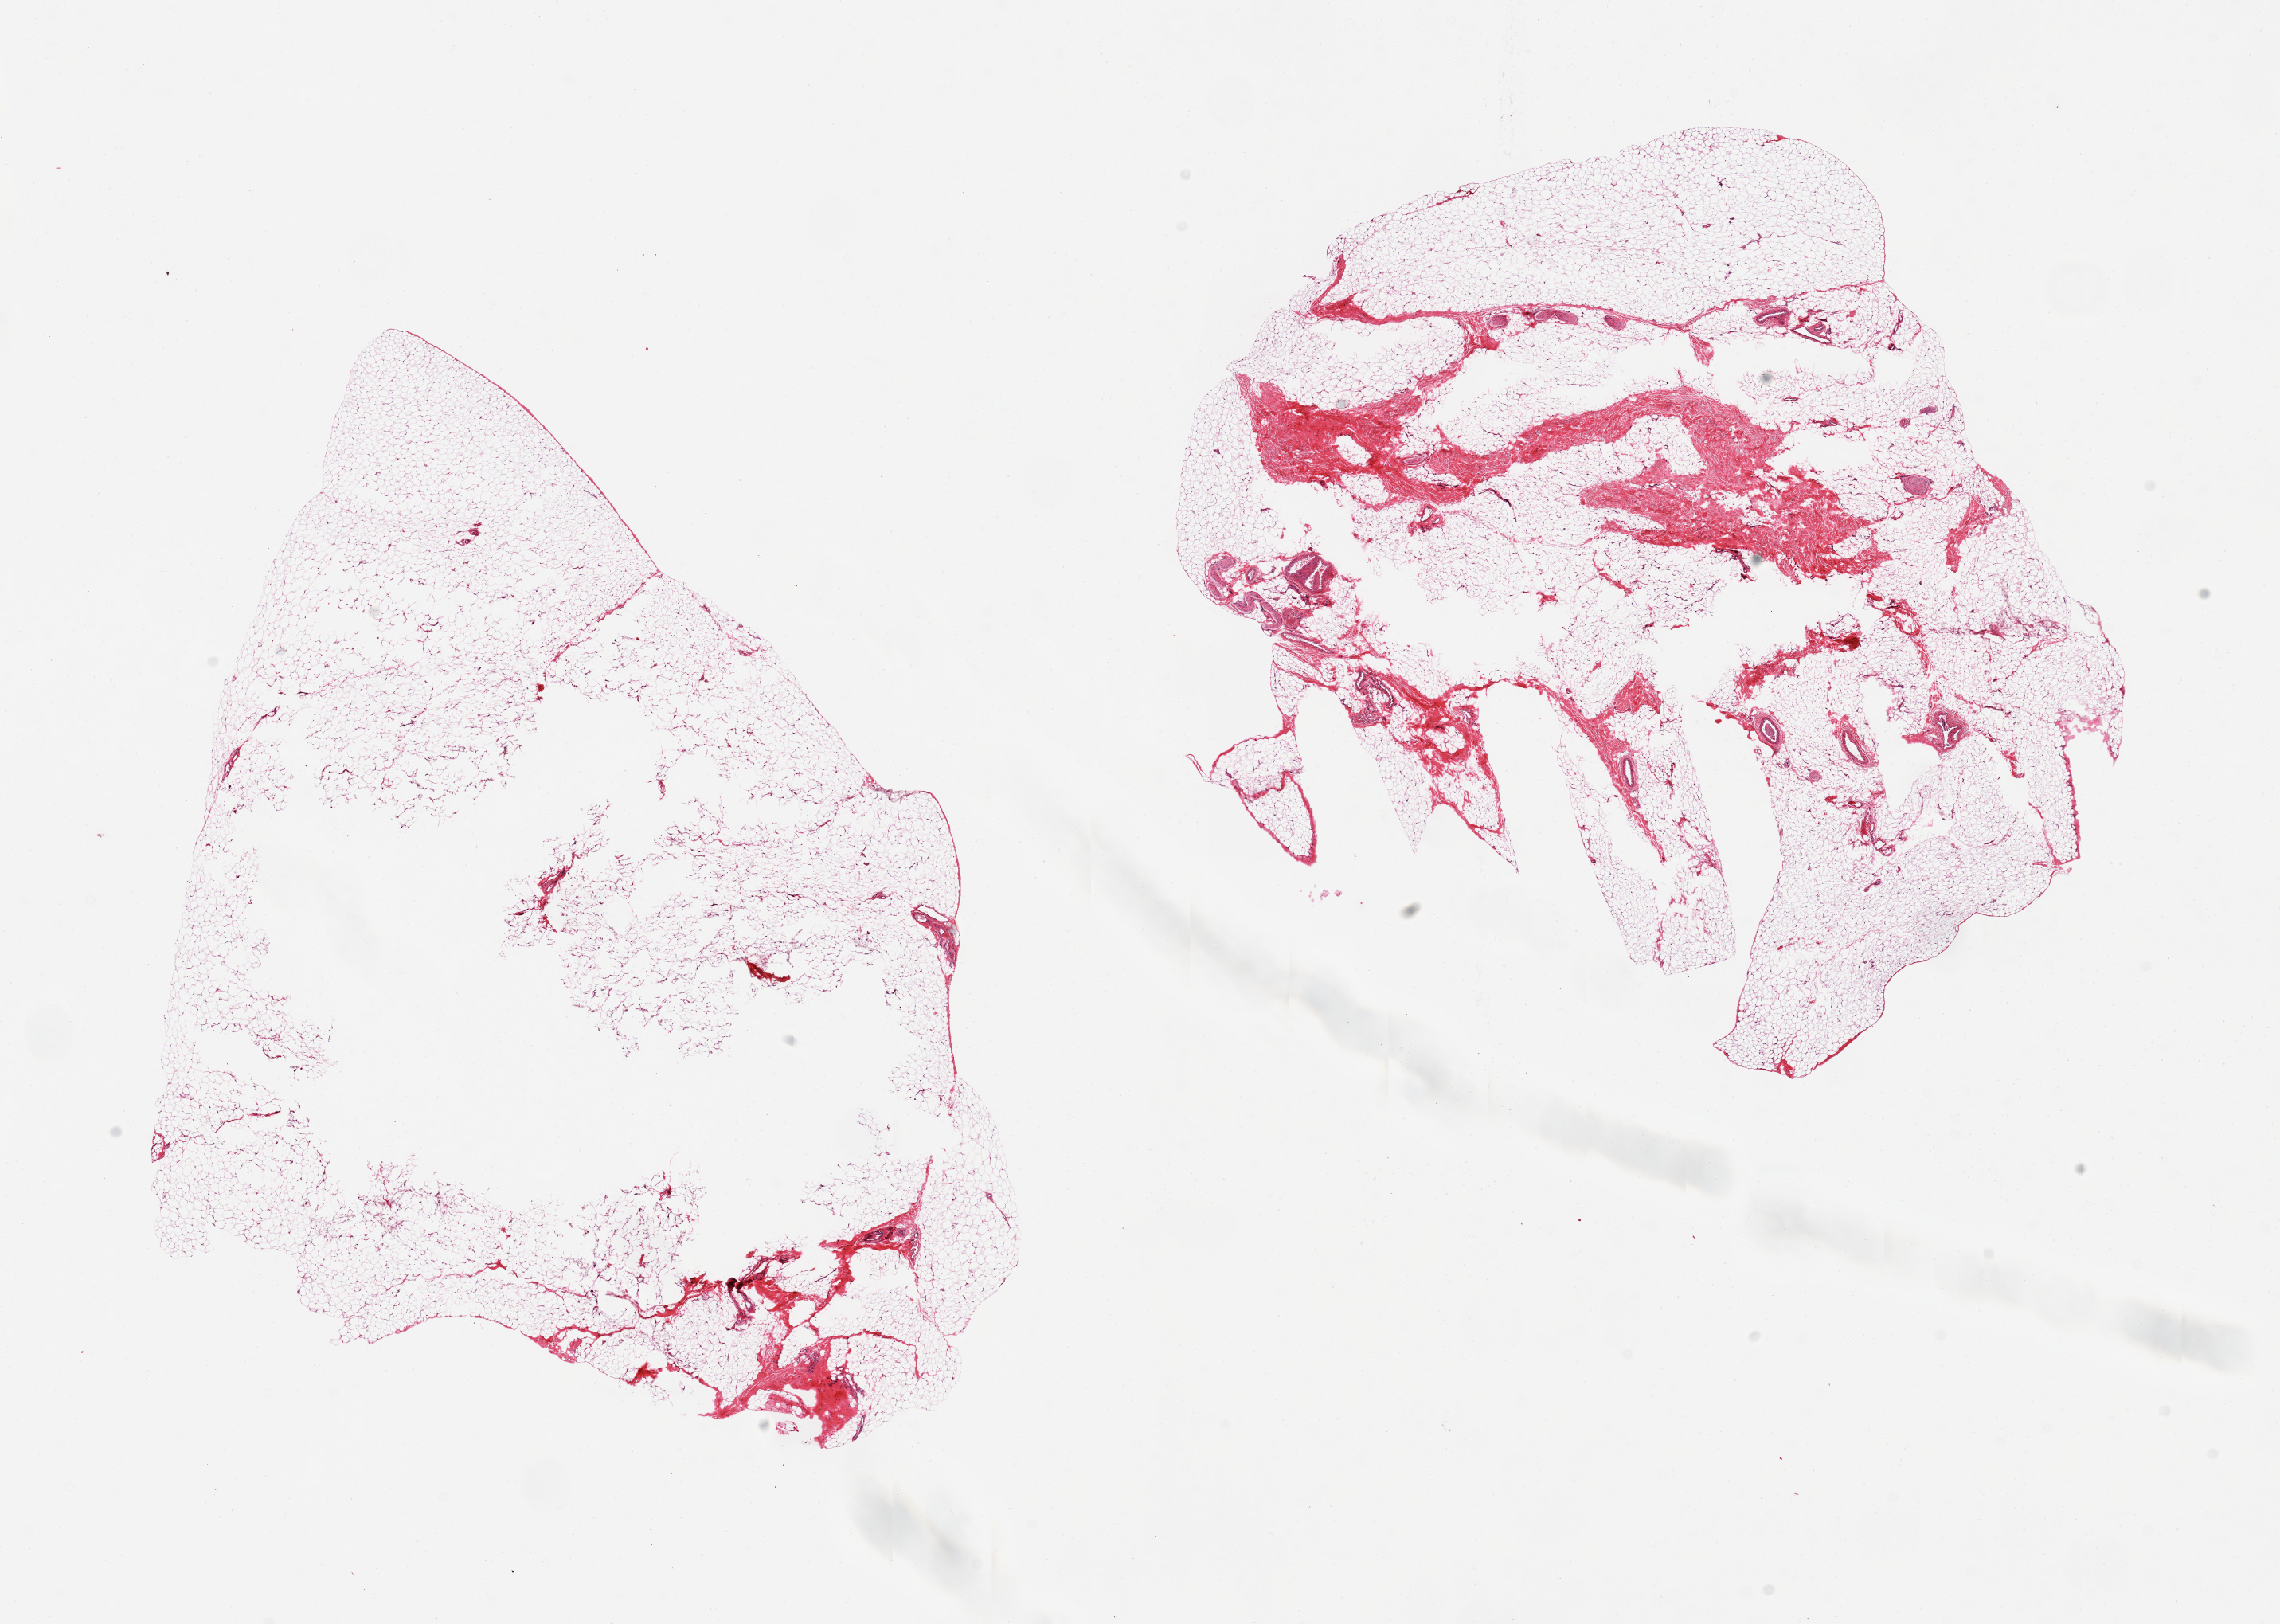
Whole-slide image, haematoxylin and eosin stain — shown as a low-resolution overview of the whole scanned area (about 22.6 x 16.1 mm). PAXgene-fixed, paraffin-embedded tissue. Target tissue: breast. Tissue donor sample.
* review note (as recorded): 2 pieces, one piece has large central defect (?poor fixation), 2nd is ~10-20% fibrous, no ductal elements noted